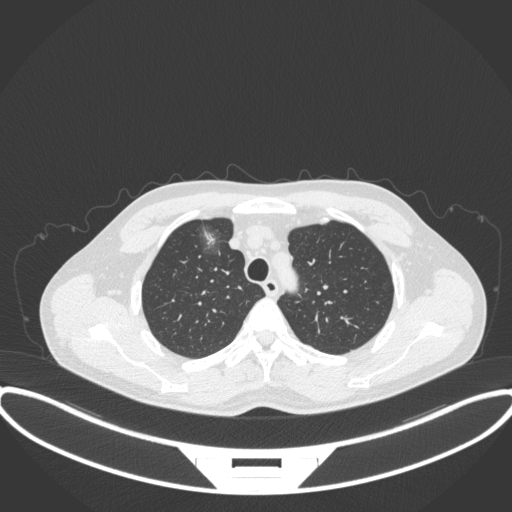
Chest CT, one axial slice; slice 291 of 395 in the series (ordered by position); reconstruction kernel B31f; lung window (W 1500 / L -600 HU); 512 × 512 image matrix. Patient: male, 60 years. From the clinical record (not read from this slice): clinical TNM (as recorded): T1c N0 M0.
Outlined on this slice (rectangle marked by the reading radiologist):
- lung tumour (recorded histology: adenocarcinoma): bounding box <195,221,229,268> (left, top, right, bottom; pixels)